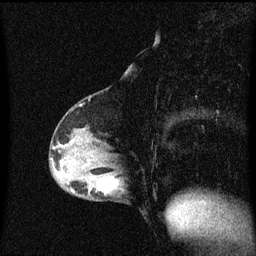
Breast MRI (dynamic contrast-enhanced), one sagittal slice. Slice 30 of 60 in the series (ordered by position). Dynamic contrast-enhanced series, image 2 of 3 at this slice position (ordered by acquisition). 1.5 T. TE 4.2 ms, TR 8.4 ms. 2 mm slice thickness. 256 × 256 image matrix, field of view 200 × 200 mm. Female patient, age 40 years.
Structures marked on this image (semi-automatically segmented with operator editing):
- analysis volume of interest (the breast-tissue region the enhancement analysis was run in; not a lesion): bounding box (x1, y1, x2, y2) in pixels: (82, 172, 126, 201)
- tumour enhancement mask (voxels above the 70 % enhancement threshold inside the analysis volume of interest): (108, 178, 118, 193)